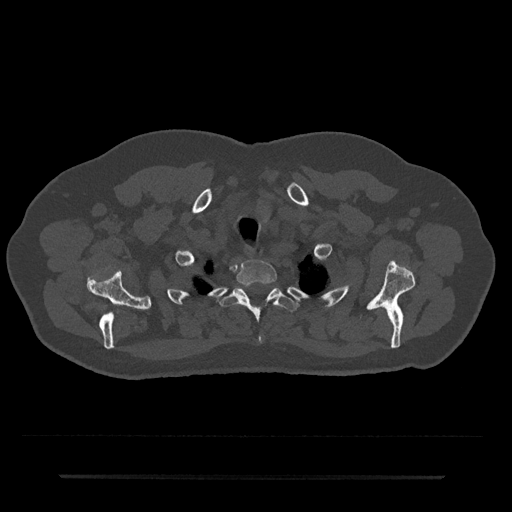
CT including the spine, one axial slice; position 618 of 797 along the scan axis; 120 kVp; bone window (W 1800 / L 400 HU); 0.5 mm slice thickness; 512 × 512 image matrix. Patient: male, 69 years. From the clinical record (not read from this slice): primary cancer: prostate.
Structures marked on this image (semi-automatically segmented with operator editing):
- T1 vertebra: bounding box (x1, y1, x2, y2) in pixels: (236, 260, 277, 286)
- T2 vertebra: (221, 288, 298, 343)